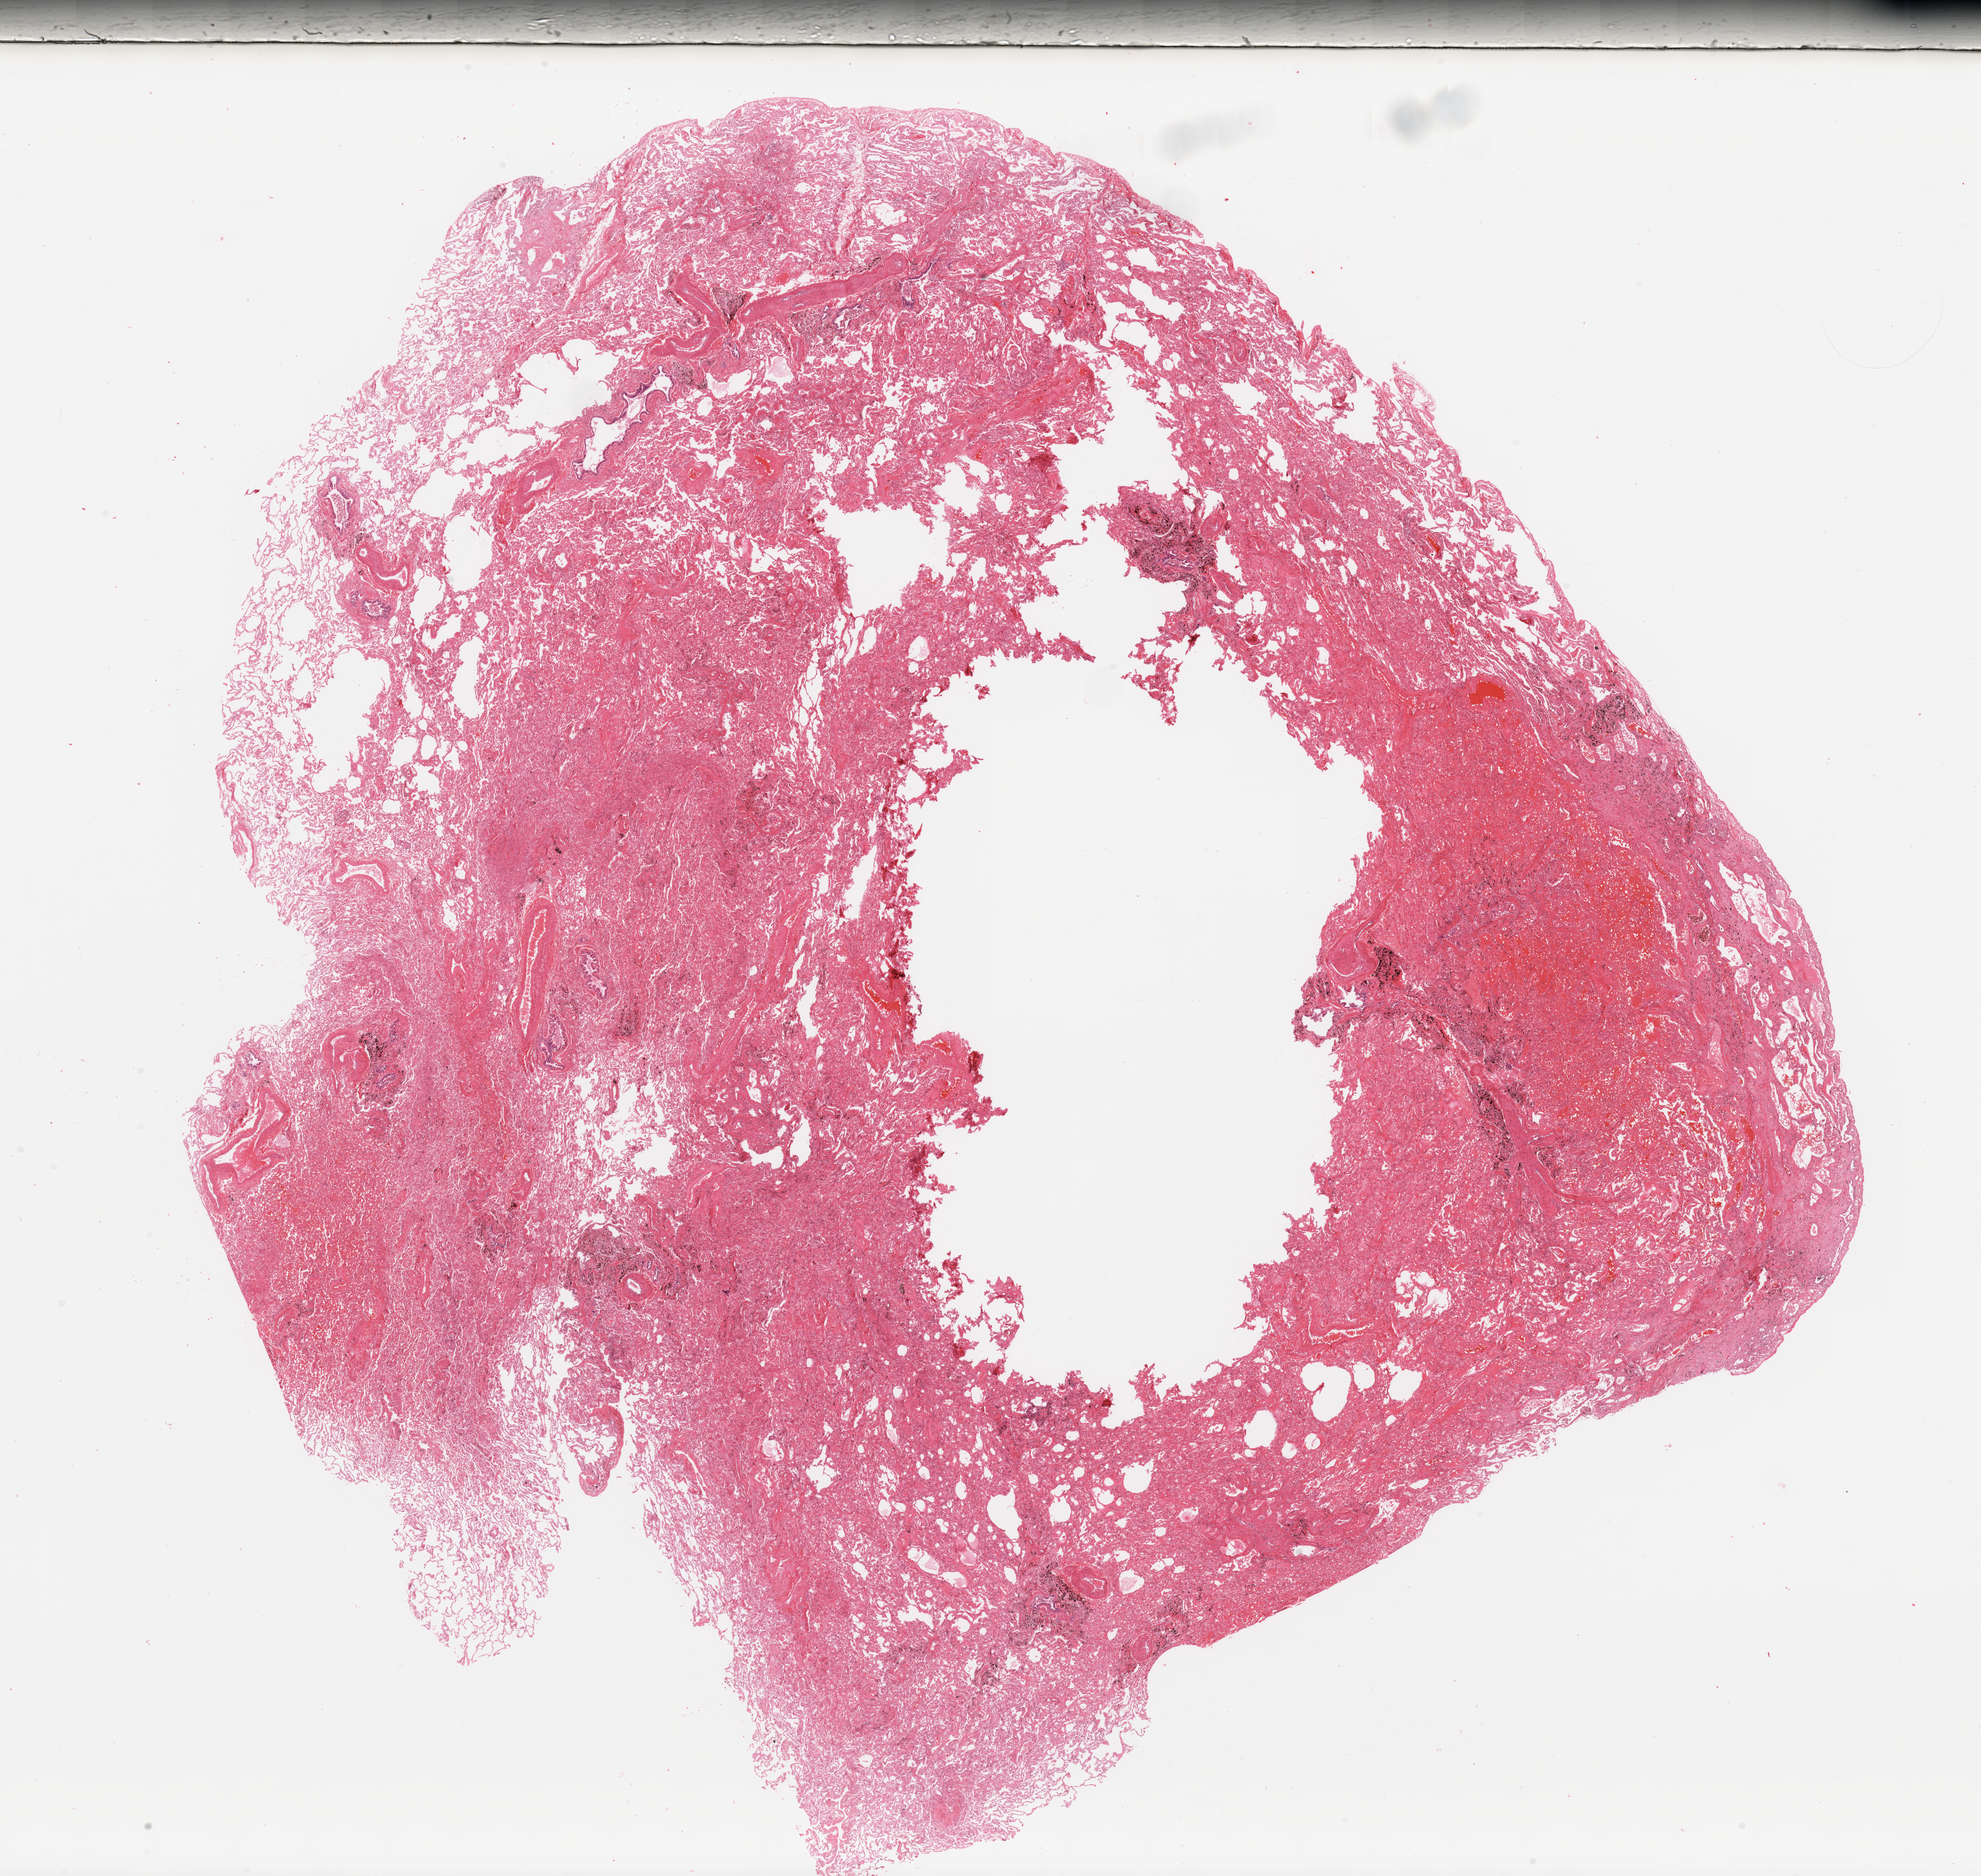
H&E whole-slide image — shown as a low-resolution overview of the whole scanned area (about 25.6 x 24.2 mm, acquisition: 20x scan); lung, normal (non-tumour) tissue. Patient: female, age 65 years.
* this section: normal (non-tumour) tissue from the same patient
* patient diagnosis: Adenocarcinoma, NOS